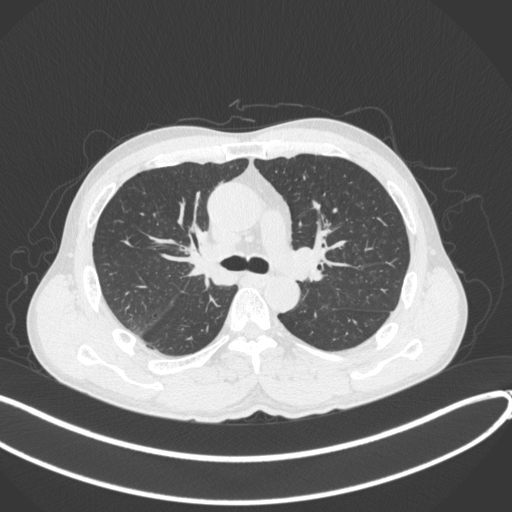
Chest CT, one axial slice; position 246 of 409 along the scan axis; reconstruction kernel B31f; 120 kVp; lung window (W 1500 / L -600 HU); 1 mm slice thickness; 512 × 512 image matrix, field of view 400 × 400 mm. Male patient, age 53 years. From the clinical record (not read from this slice): clinical TNM (as recorded): T1b N0 M0.
Structures marked on this image (rectangle marked by the reading radiologist):
- lung tumour (recorded histology: squamous cell carcinoma): box from (x=176, y=234) to (x=237, y=288) px